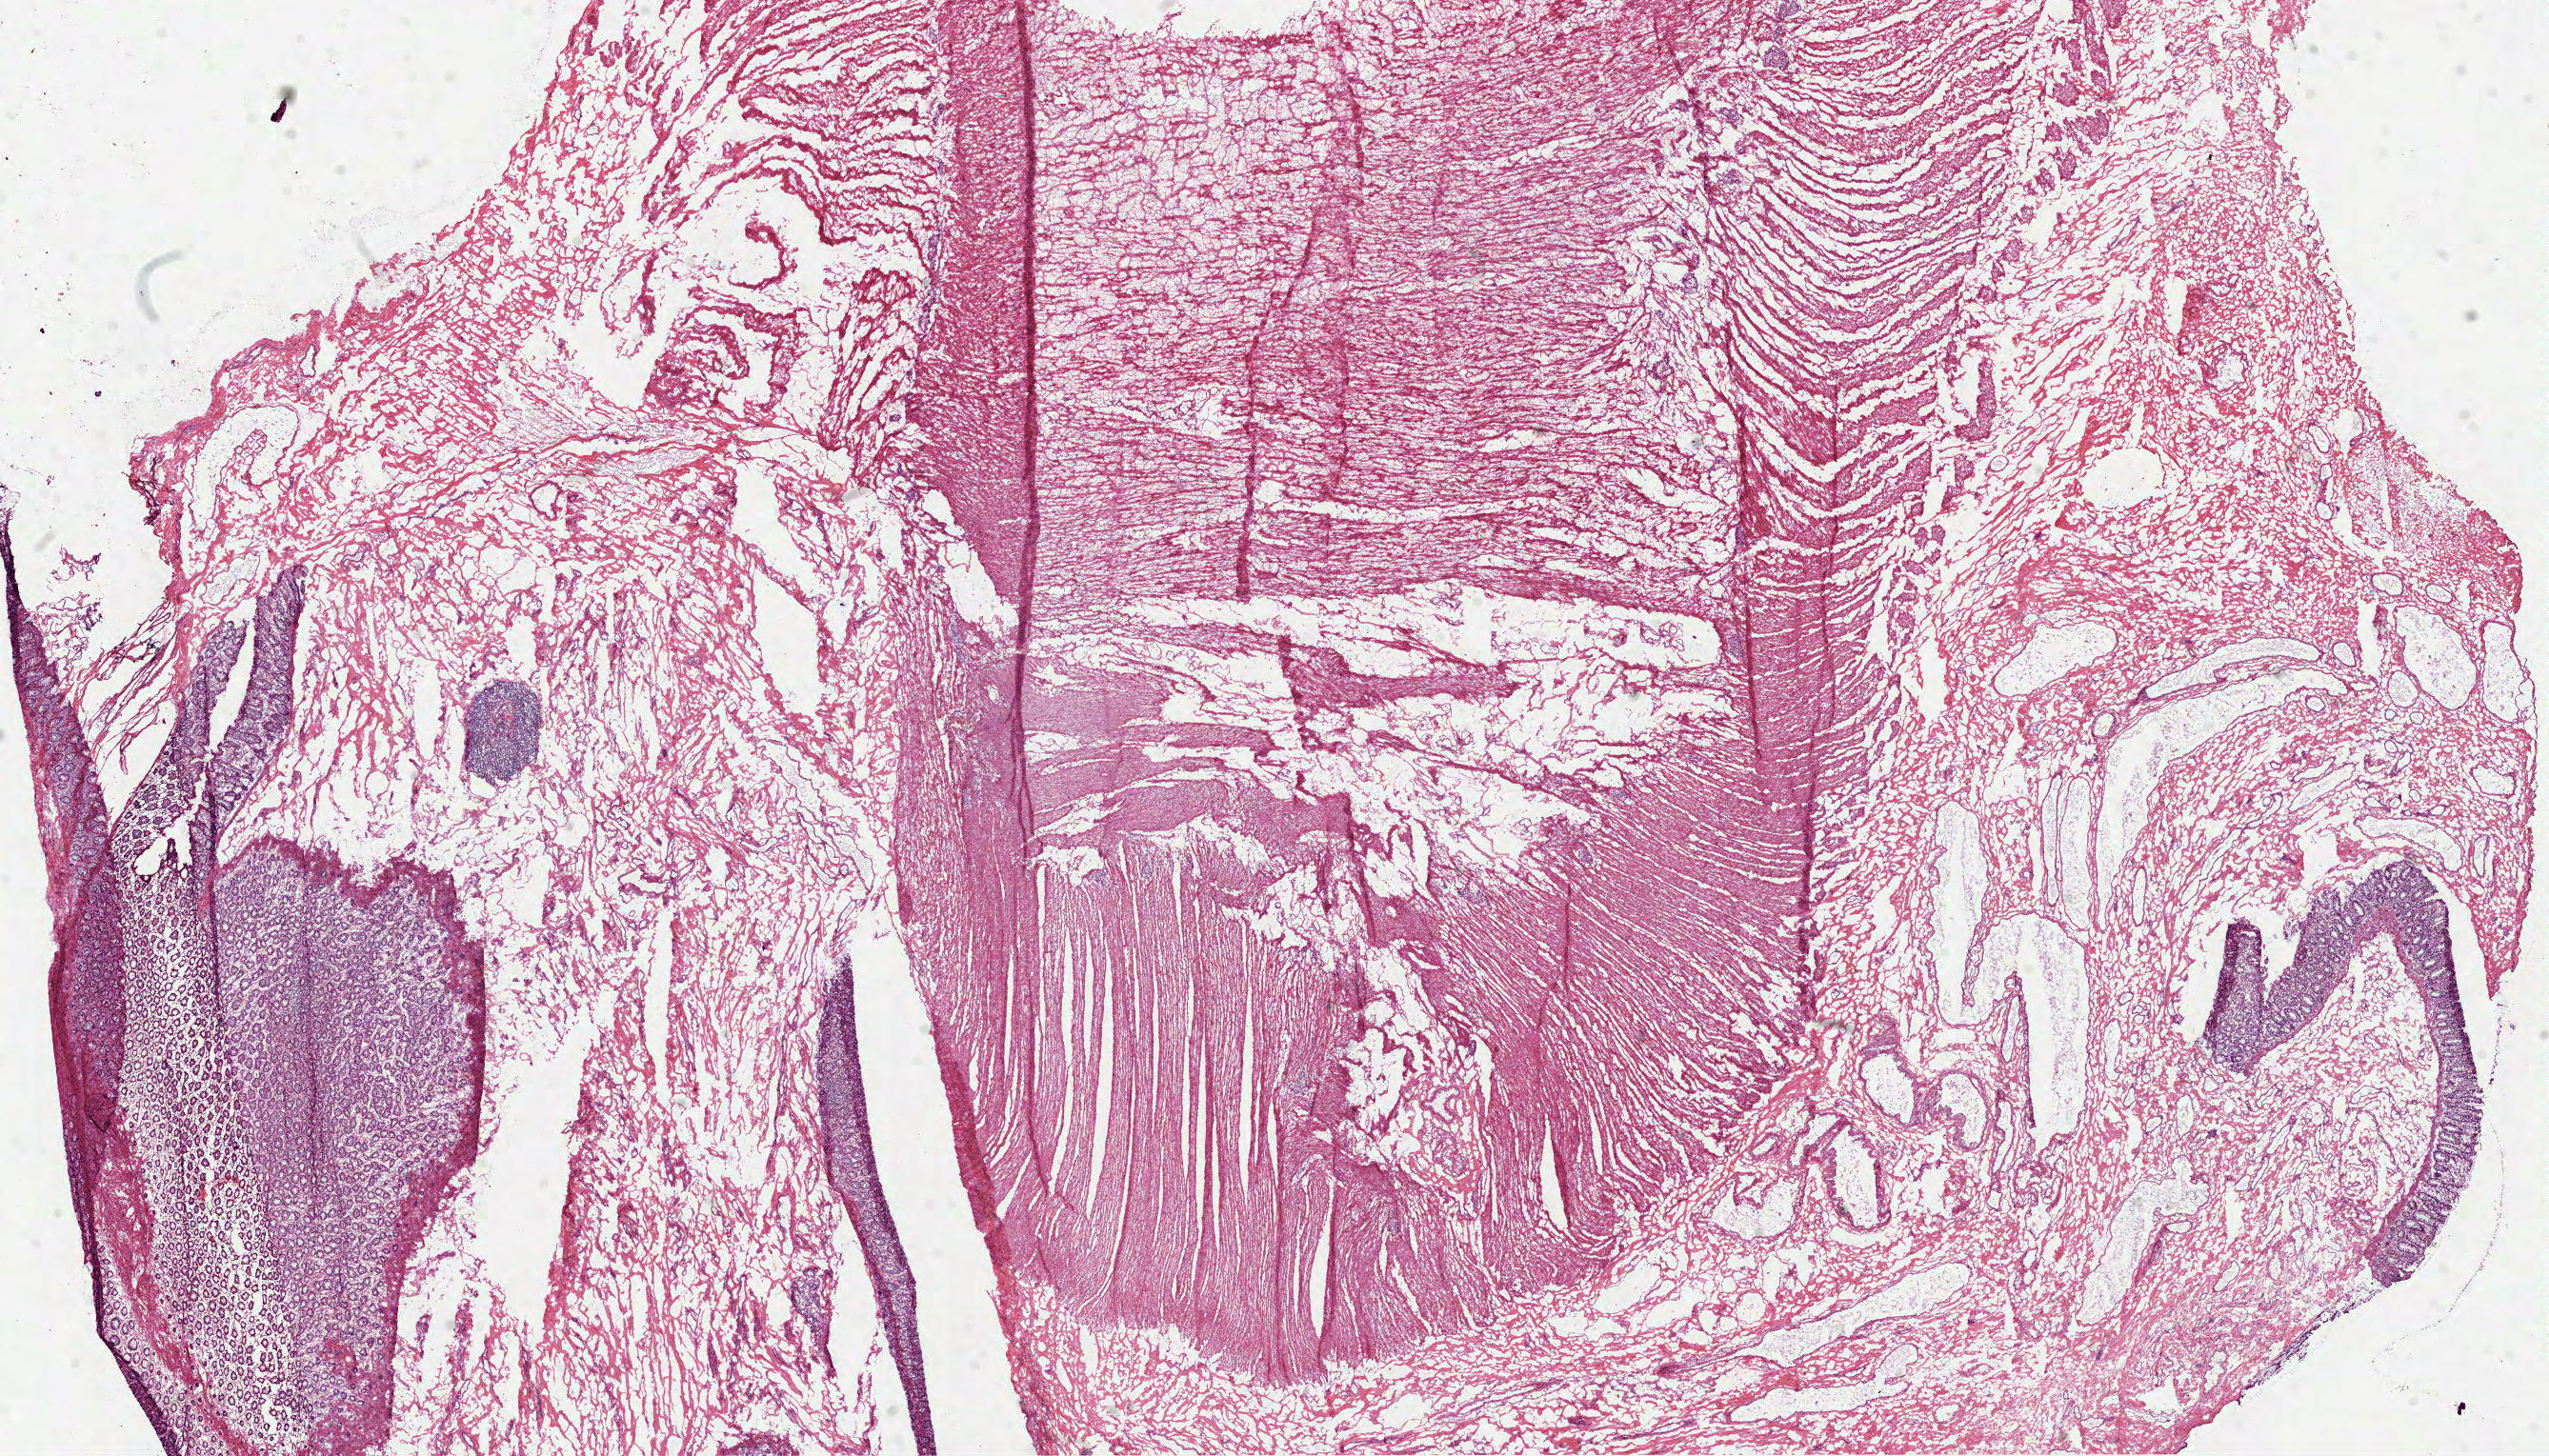
Whole-slide histology image, Hematoxylin and eosin (H&E) stained, shown as a low-resolution overview of the whole scanned area (about 21.6 x 12.3 mm, from a 40x scan). Frozen section from the top of the tissue portion. Colon, solid tissue normal (non-tumour tissue) sample. Male, age 77 years at initial diagnosis.
This section: solid tissue normal (non-tumour) sample from the same patient. Patient diagnosis: Adenocarcinoma, NOS (ascending colon).